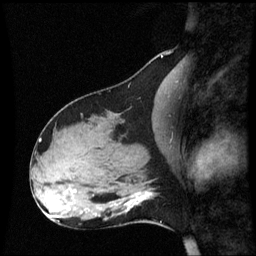
Breast MRI (dynamic contrast-enhanced), one sagittal slice. Position 25 of 60 along the scan axis. Dynamic contrast-enhanced series, image 2 of 3 at this slice position (ordered by acquisition). 1.5 T. TE 4.2 ms, TR 8.9 ms. 256 × 256 image matrix, field of view 220 × 220 mm. Patient: female, 31 years. Case-level facts recorded for this patient, not image findings: setting: breast cancer imaged before/during neoadjuvant chemotherapy; receptor status: HR-positive, HER2-negative.
Outlined on this slice (semi-automatic segmentation, software-assisted and operator-edited):
- analysis volume of interest (the breast-tissue region the enhancement analysis was run in; not a lesion): bounding box <109,180,159,227> (left, top, right, bottom; pixels)
- tumour enhancement mask (voxels above the 70 % enhancement threshold inside the analysis volume of interest): <127,208,129,211>